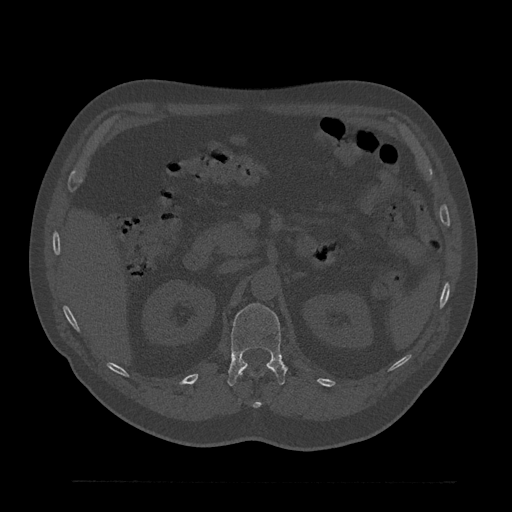
CT including the spine, one axial slice; slice 184 of 797 in the series (ordered by position); 120 kVp; bone window (W 1800 / L 400 HU); 512 × 512 image matrix, field of view 430 × 430 mm. Male patient, age 61 years. From the clinical record (not read from this slice): primary cancer: prostate.
Annotated regions visible in this slice (semi-automatic segmentation, software-assisted and operator-edited):
- L1 vertebra: box from (x=227, y=304) to (x=287, y=386) px
- T12 vertebra: (x=253, y=402)–(x=262, y=408)